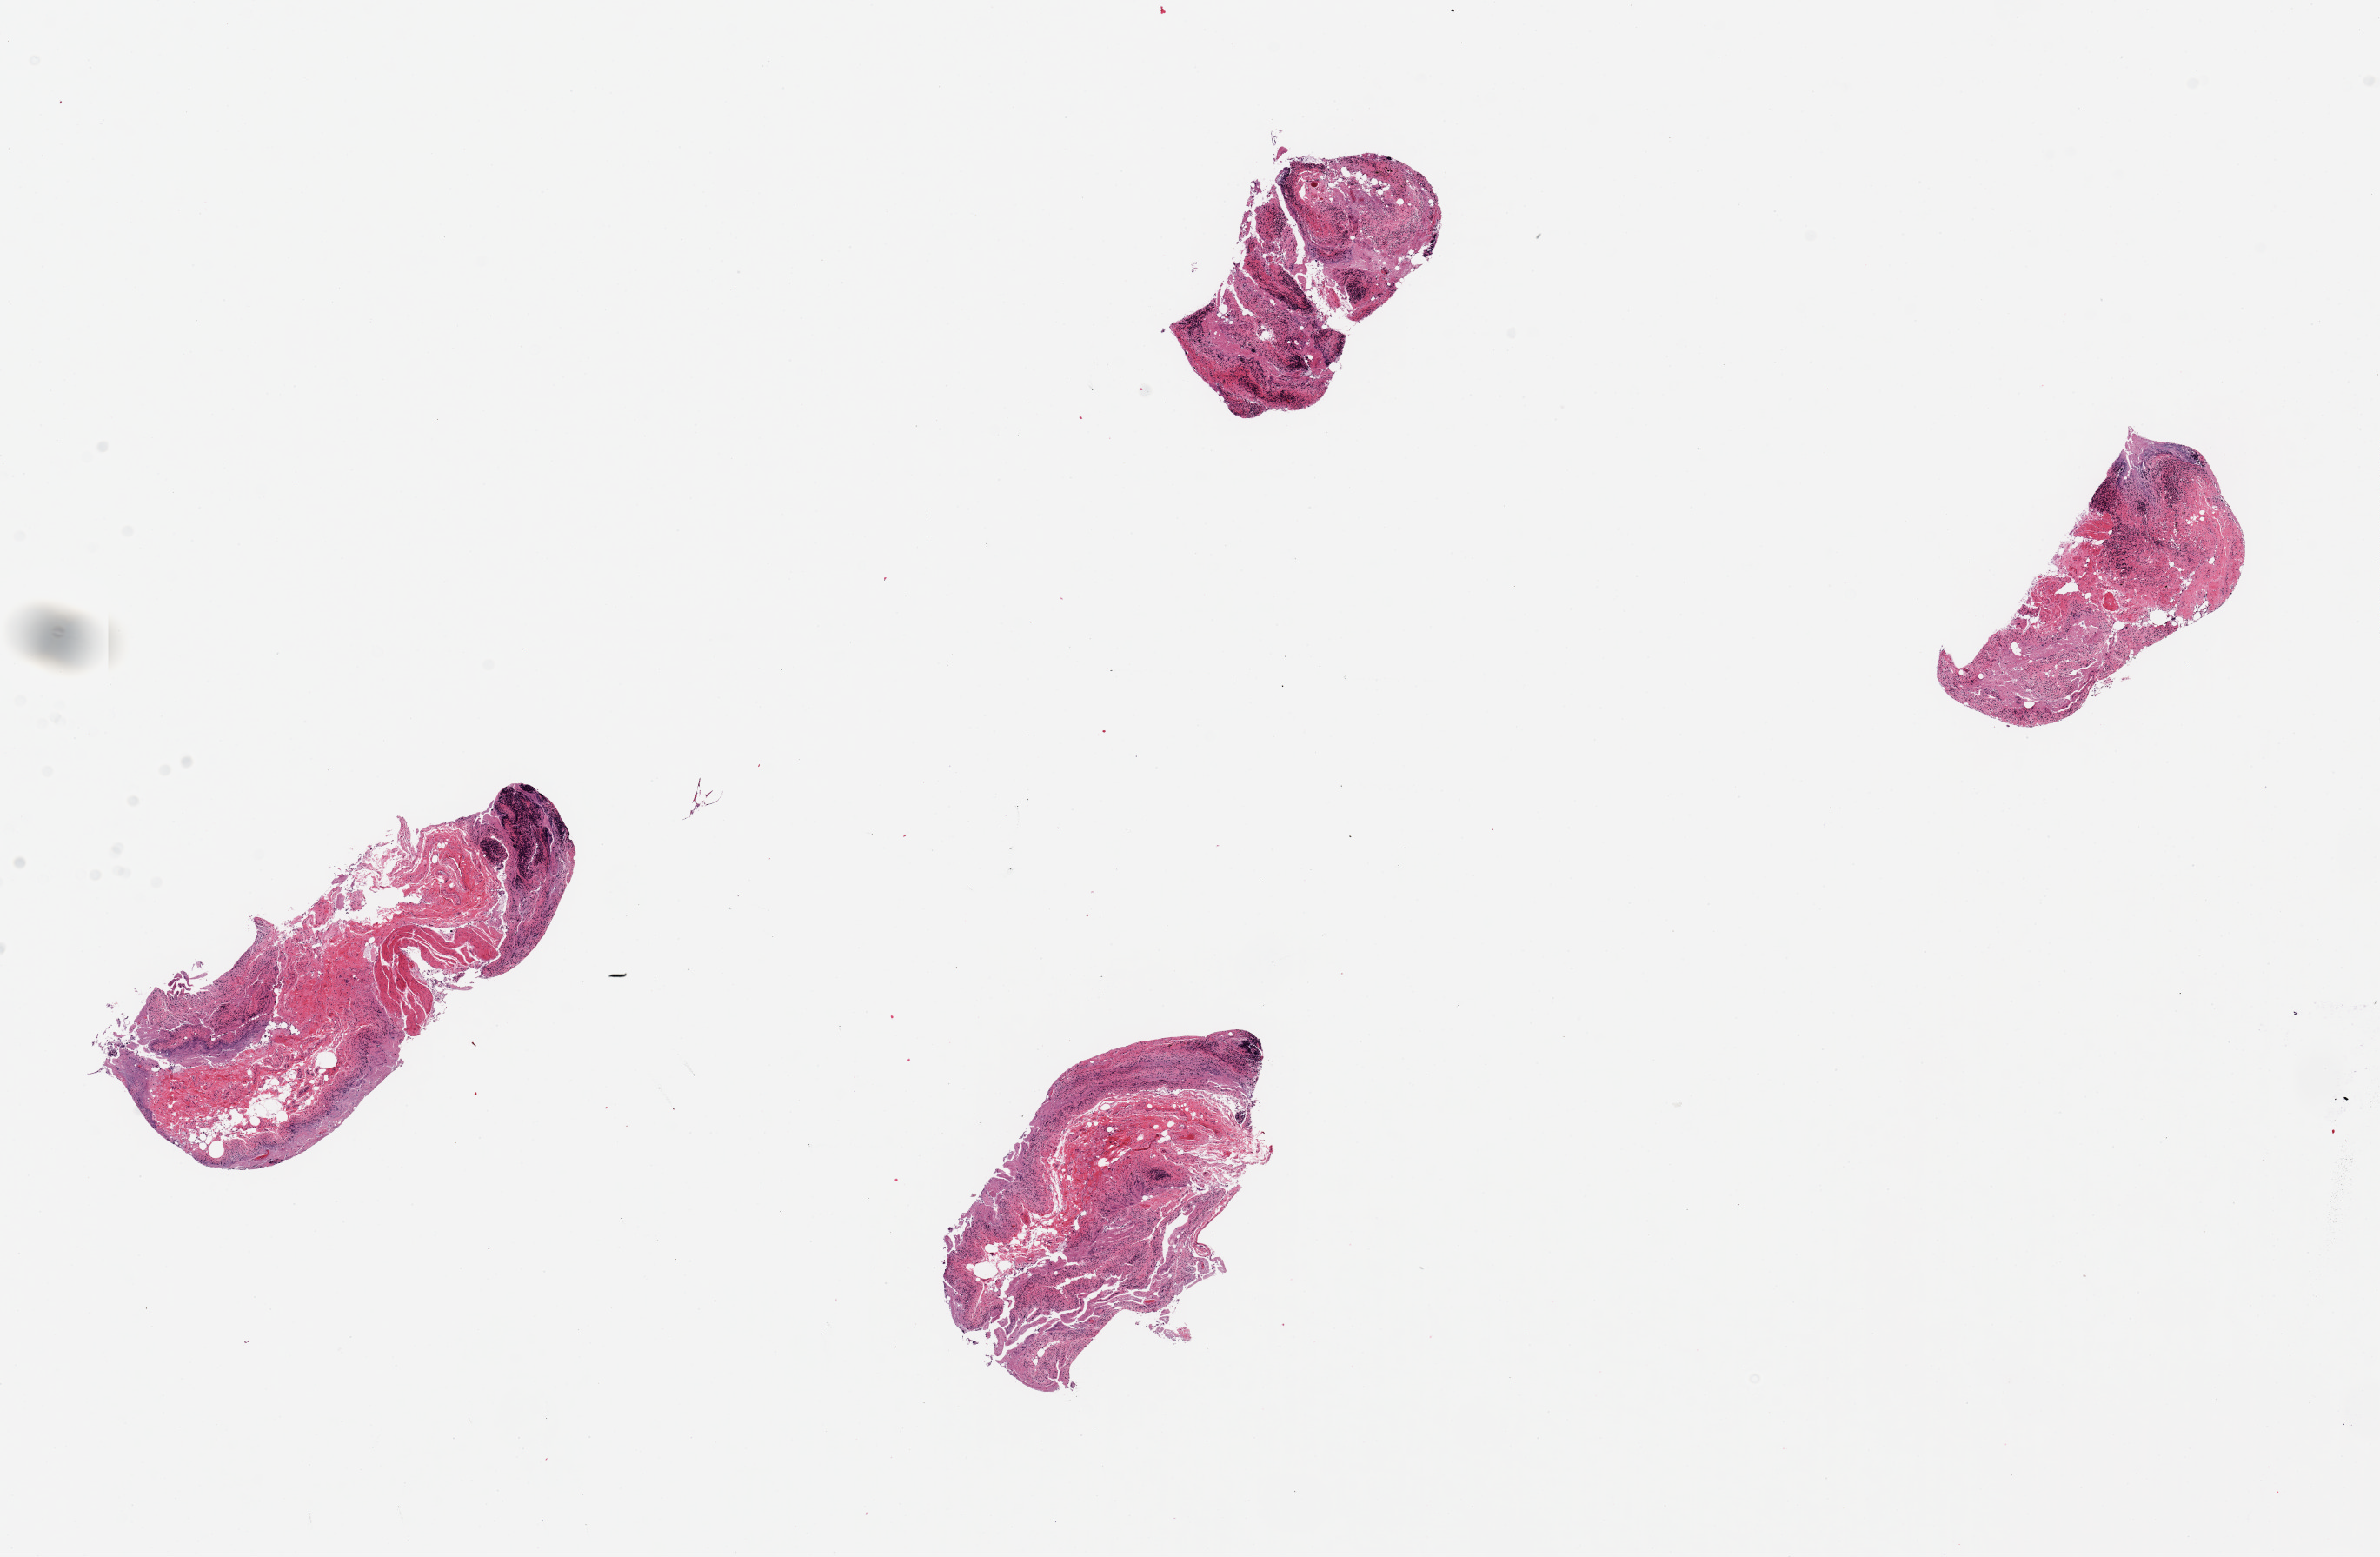
Digitized haematoxylin and eosin-stained section — shown as a low-resolution overview of the whole scanned area (about 21.7 x 14.2 mm, from a 20x scan), PAXgene-fixed paraffin-embedded (PFPE) section, target tissue: ileum, donor tissue sample. Donor: female.
Review note (as recorded): 4 pieces, up to 5x2mm; mucosa and lymphoid tissue autolyzed; well trimmed from muscularis.